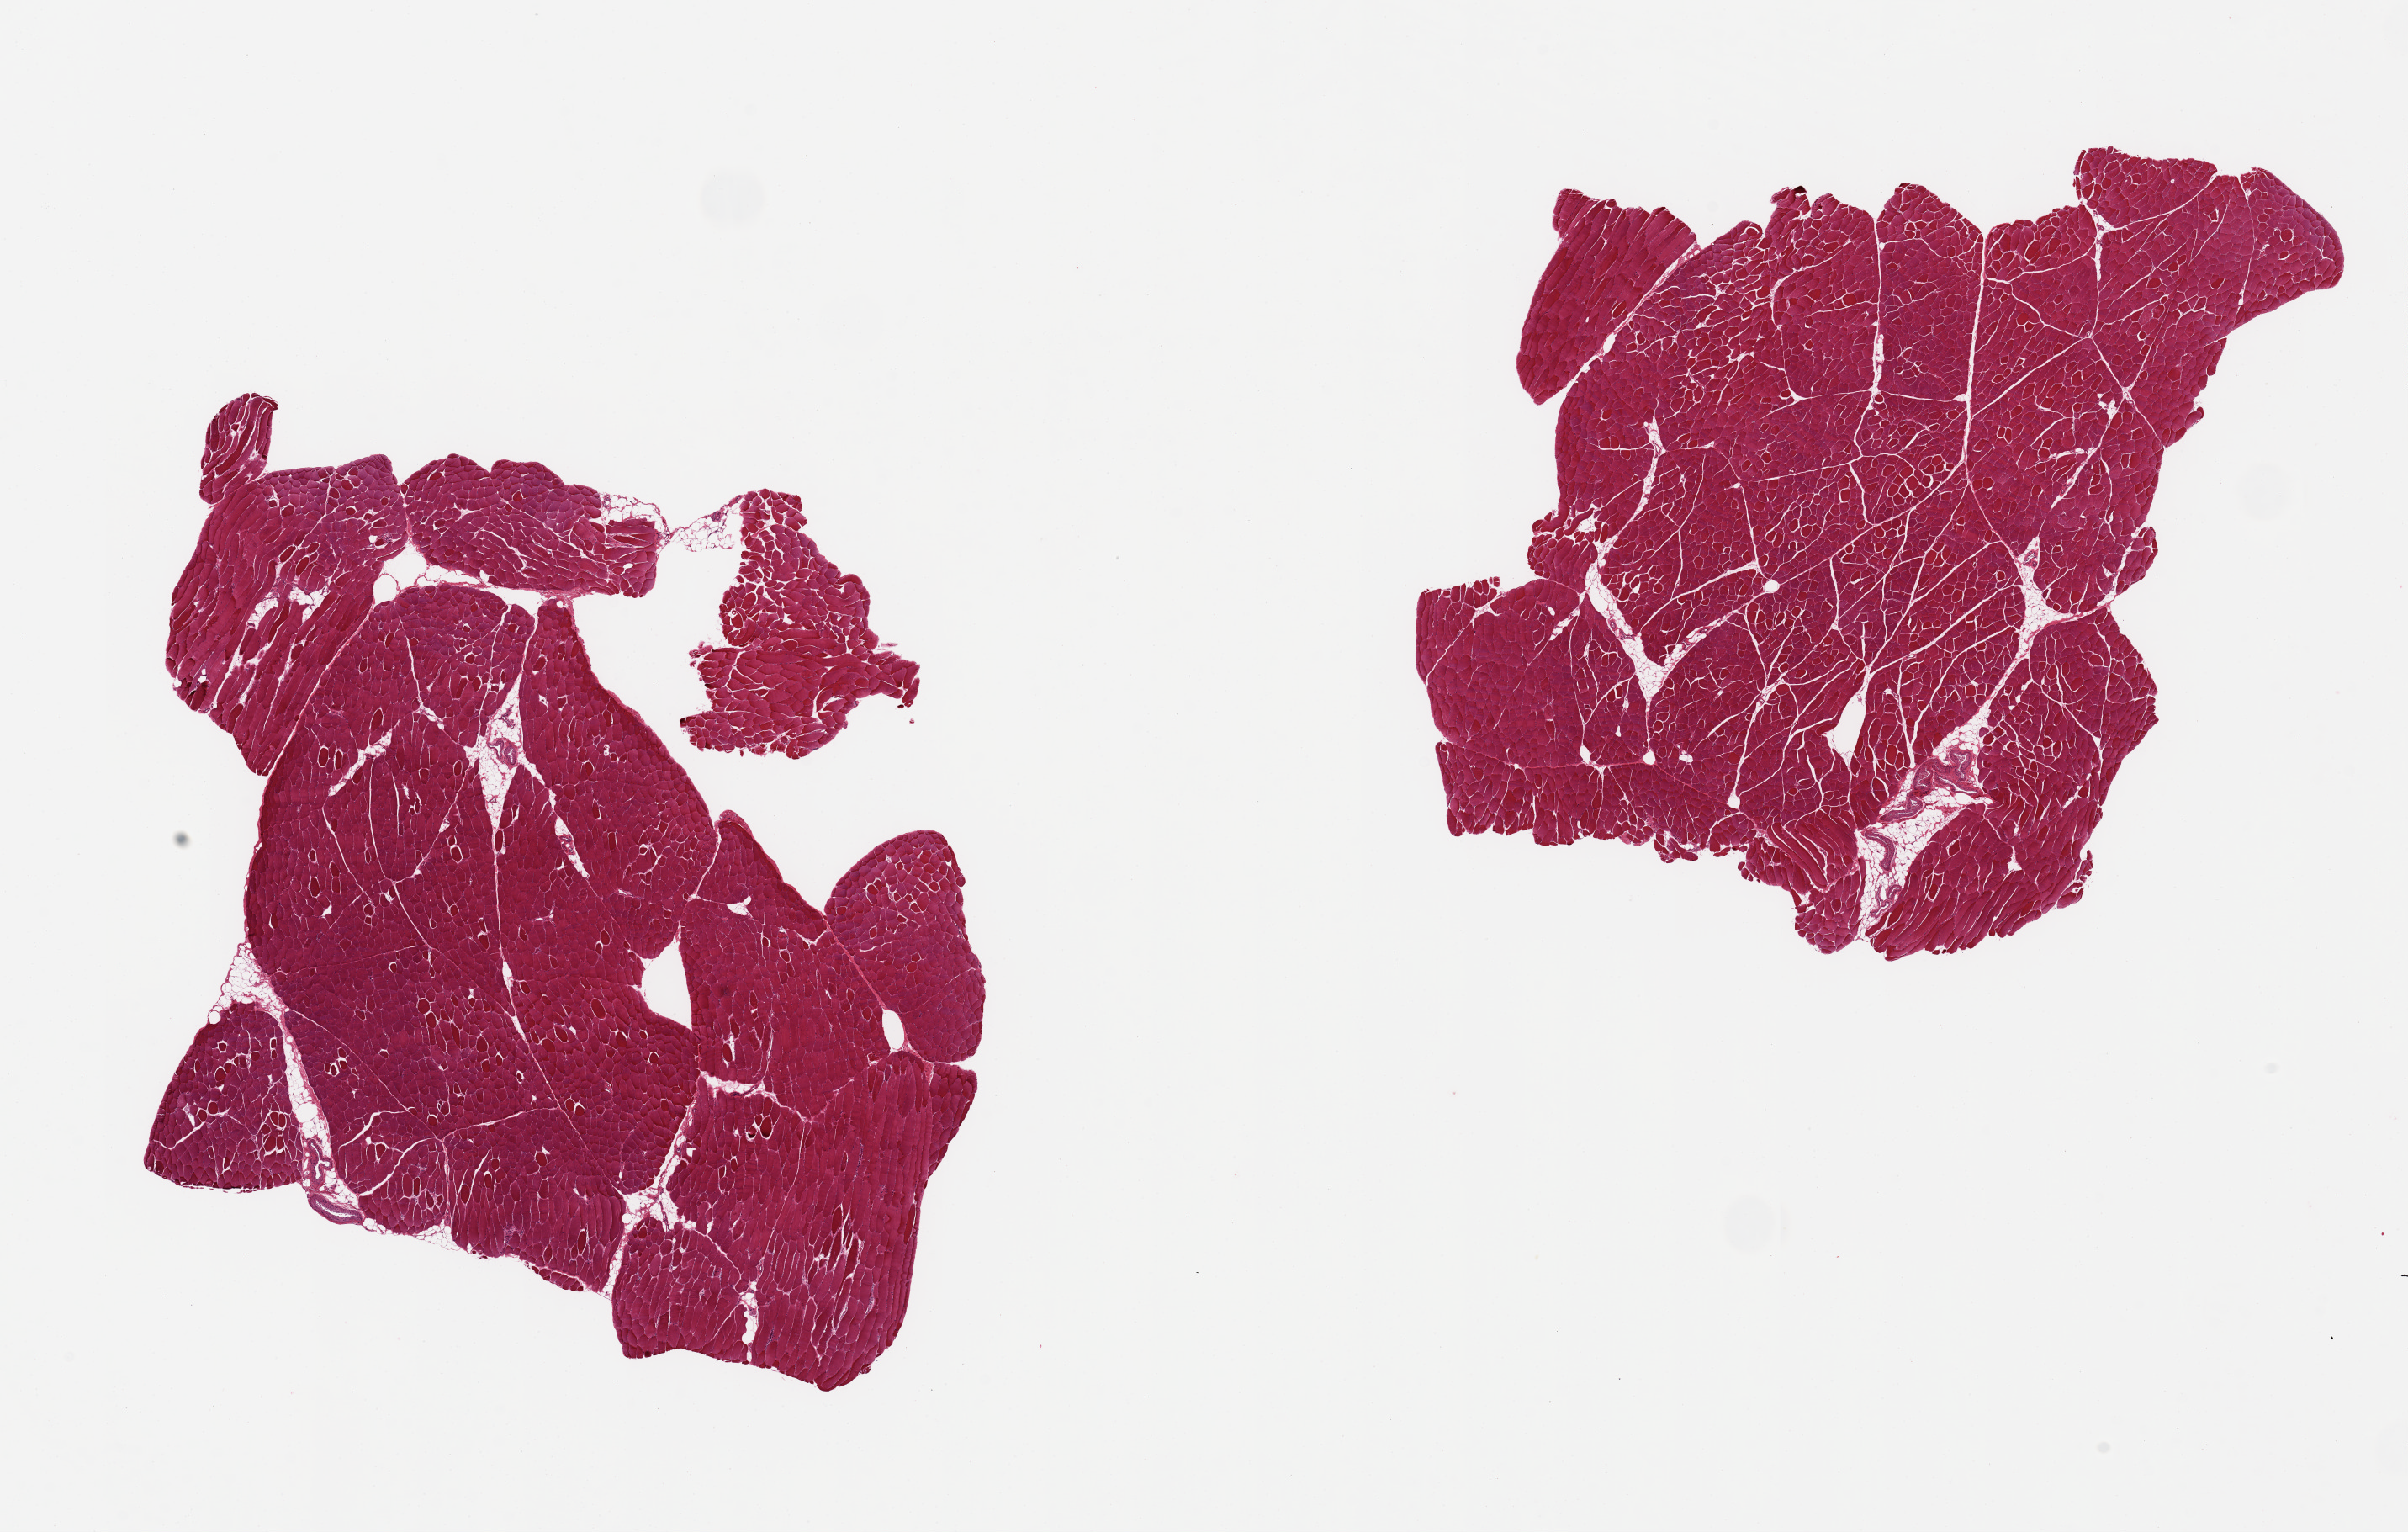
Digitized H&E-stained section — whole scanned area (about 22.6 x 14.4 mm, from a 20x scan) shown as a low-resolution overview, PAXgene-fixed paraffin-embedded (PFPE) section, target tissue: skeletal muscle, donor tissue sample. Donor sex: female.
• reviewer comment on this tissue sample: 2 pieces, minimal interstitial fat